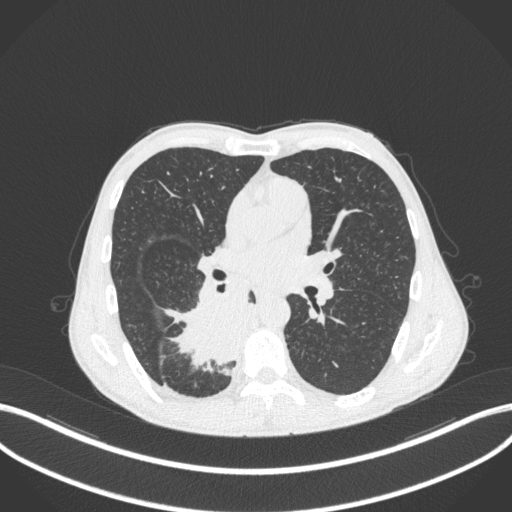
Chest CT, one axial slice; position 197 of 371 along the scan axis; reconstruction kernel B31f; lung window (W 1500 / L -600 HU); 512 × 512 image matrix, field of view 400 × 400 mm. Male patient, age 58 years. Case-level facts recorded for this patient, not image findings: clinical TNM (as recorded): T3 N1 M1.
Annotated regions visible in this slice (rectangle marked by the reading radiologist):
- lung tumour (recorded histology: squamous cell carcinoma): box from (x=155, y=294) to (x=257, y=373) px